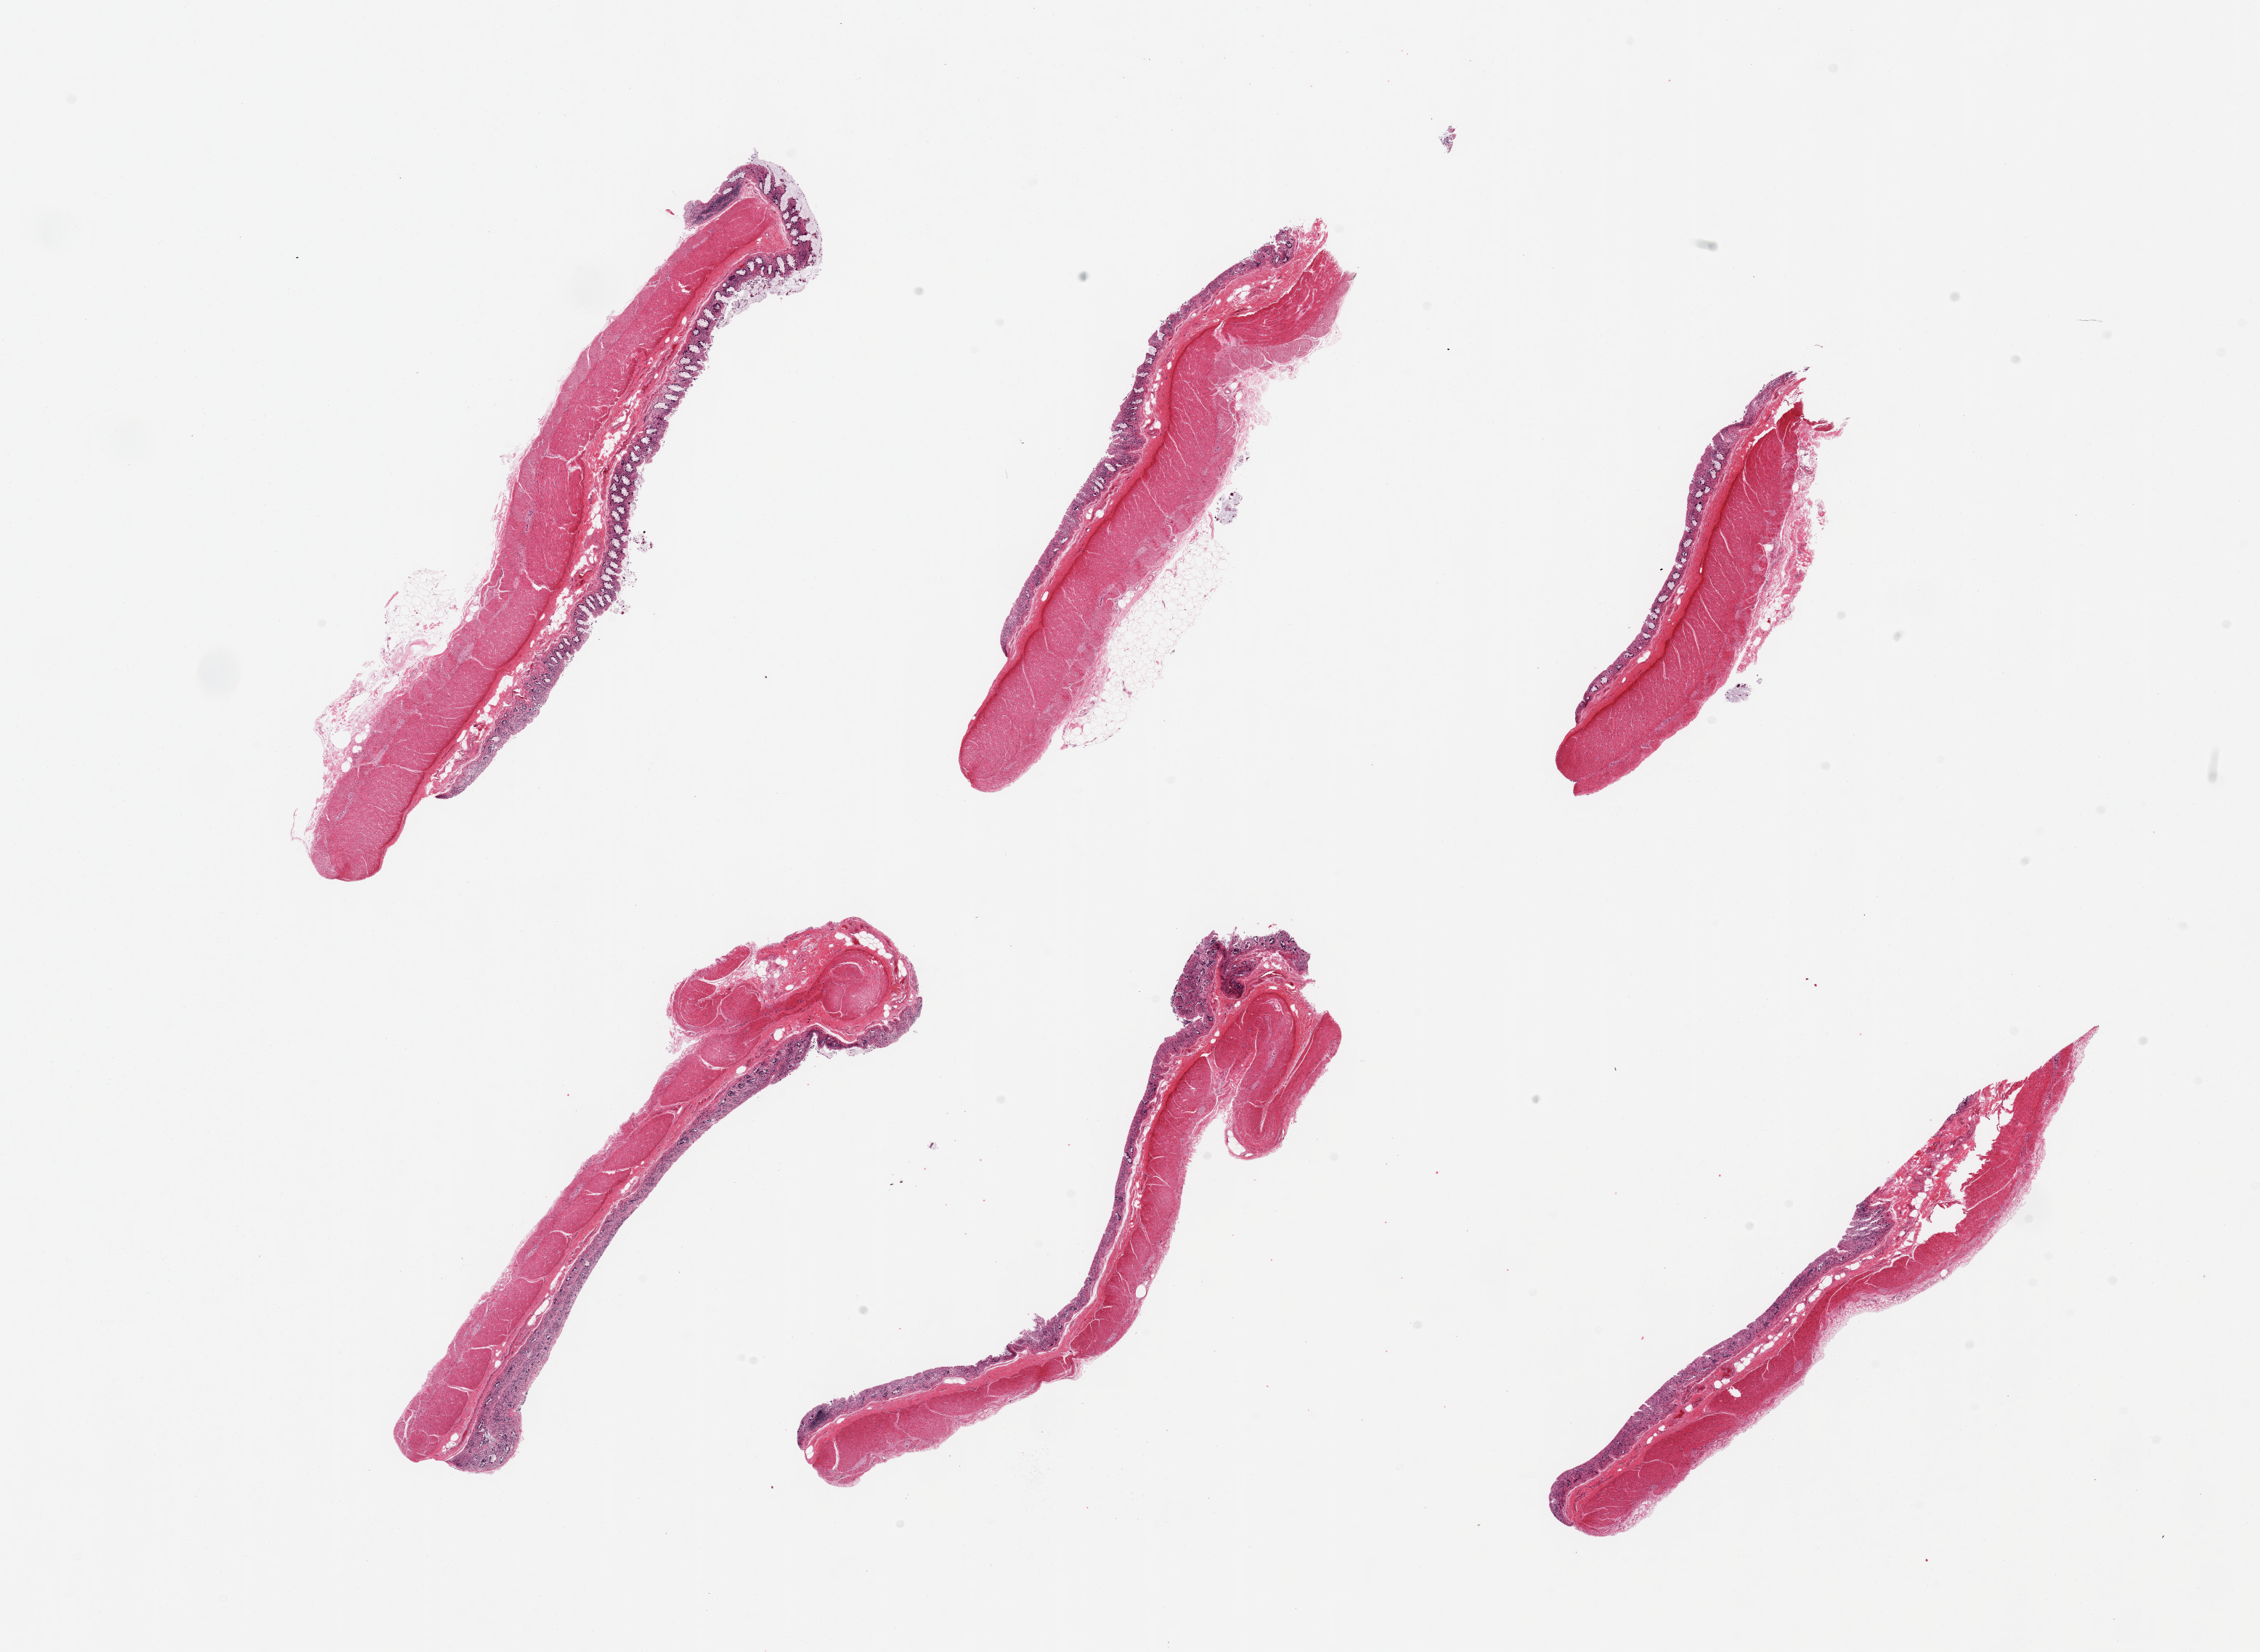
Whole-slide image, hematoxylin and eosin (H&E) stain — whole scanned area (about 24.6 x 18.0 mm) shown as a low-resolution overview, PAXgene-fixed paraffin-embedded (PFPE) section, sampled site (target tissue): transverse colon, tissue donor sample. Donor: male.
Pathologist's review note for this sample: 6 pieces target mucosa up to ~0.35mm, variably moderately autolyzed, ~30% thickness.